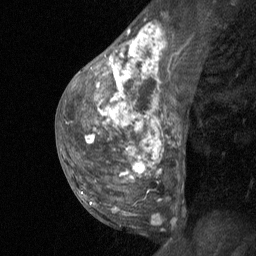
Breast MRI (dynamic contrast-enhanced), one sagittal slice. Position 35 of 64 along the scan axis. Dynamic contrast-enhanced study with each time point stored as its own series, time point 2 of 3 at this slice position (early post-contrast, ordered by acquisition time). 1.5 T. TE 4.8 ms, TR 27 ms. 256 × 256 image matrix. Patient: female, 36 years. From the clinical record (not read from this slice): setting: breast cancer imaged before/during neoadjuvant chemotherapy; receptor status: HR-positive, HER2-negative.
Annotated regions visible in this slice (semi-automatically segmented with operator editing):
- analysis volume of interest (the breast-tissue region the enhancement analysis was run in; not a lesion): bounding box [x1, y1, x2, y2] px = [67, 12, 176, 235]
- tumour enhancement mask (voxels above the 90 % enhancement threshold inside the analysis volume of interest): [85, 26, 153, 178]